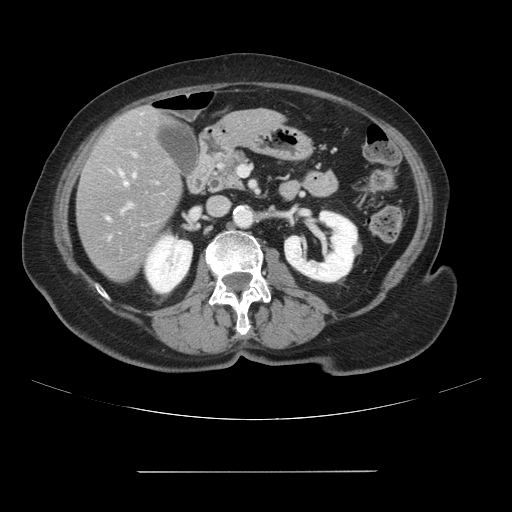
Contrast-enhanced abdominal CT, one axial slice. Position 34 of 111 along the scan axis. 120 kVp. Intravenous contrast given. Soft-tissue window (W 400 / L 40 HU). 2.5 mm slice thickness. 512 × 512 image matrix. Female patient, age 74 years. Case-level facts recorded for this patient, not image findings: diagnosis: colorectal cancer liver metastases, imaged before liver resection; multiple liver metastases: yes; largest metastasis: 1.1 cm; disease in both lobes: yes.
Outlined on this slice (manually delineated by an expert):
- hepatic veins: bounding box (x1, y1, x2, y2) in pixels: (121, 174, 127, 185)
- liver: (77, 107, 279, 282)
- planned liver remnant (the part of the liver to remain after resection): (140, 106, 260, 133)